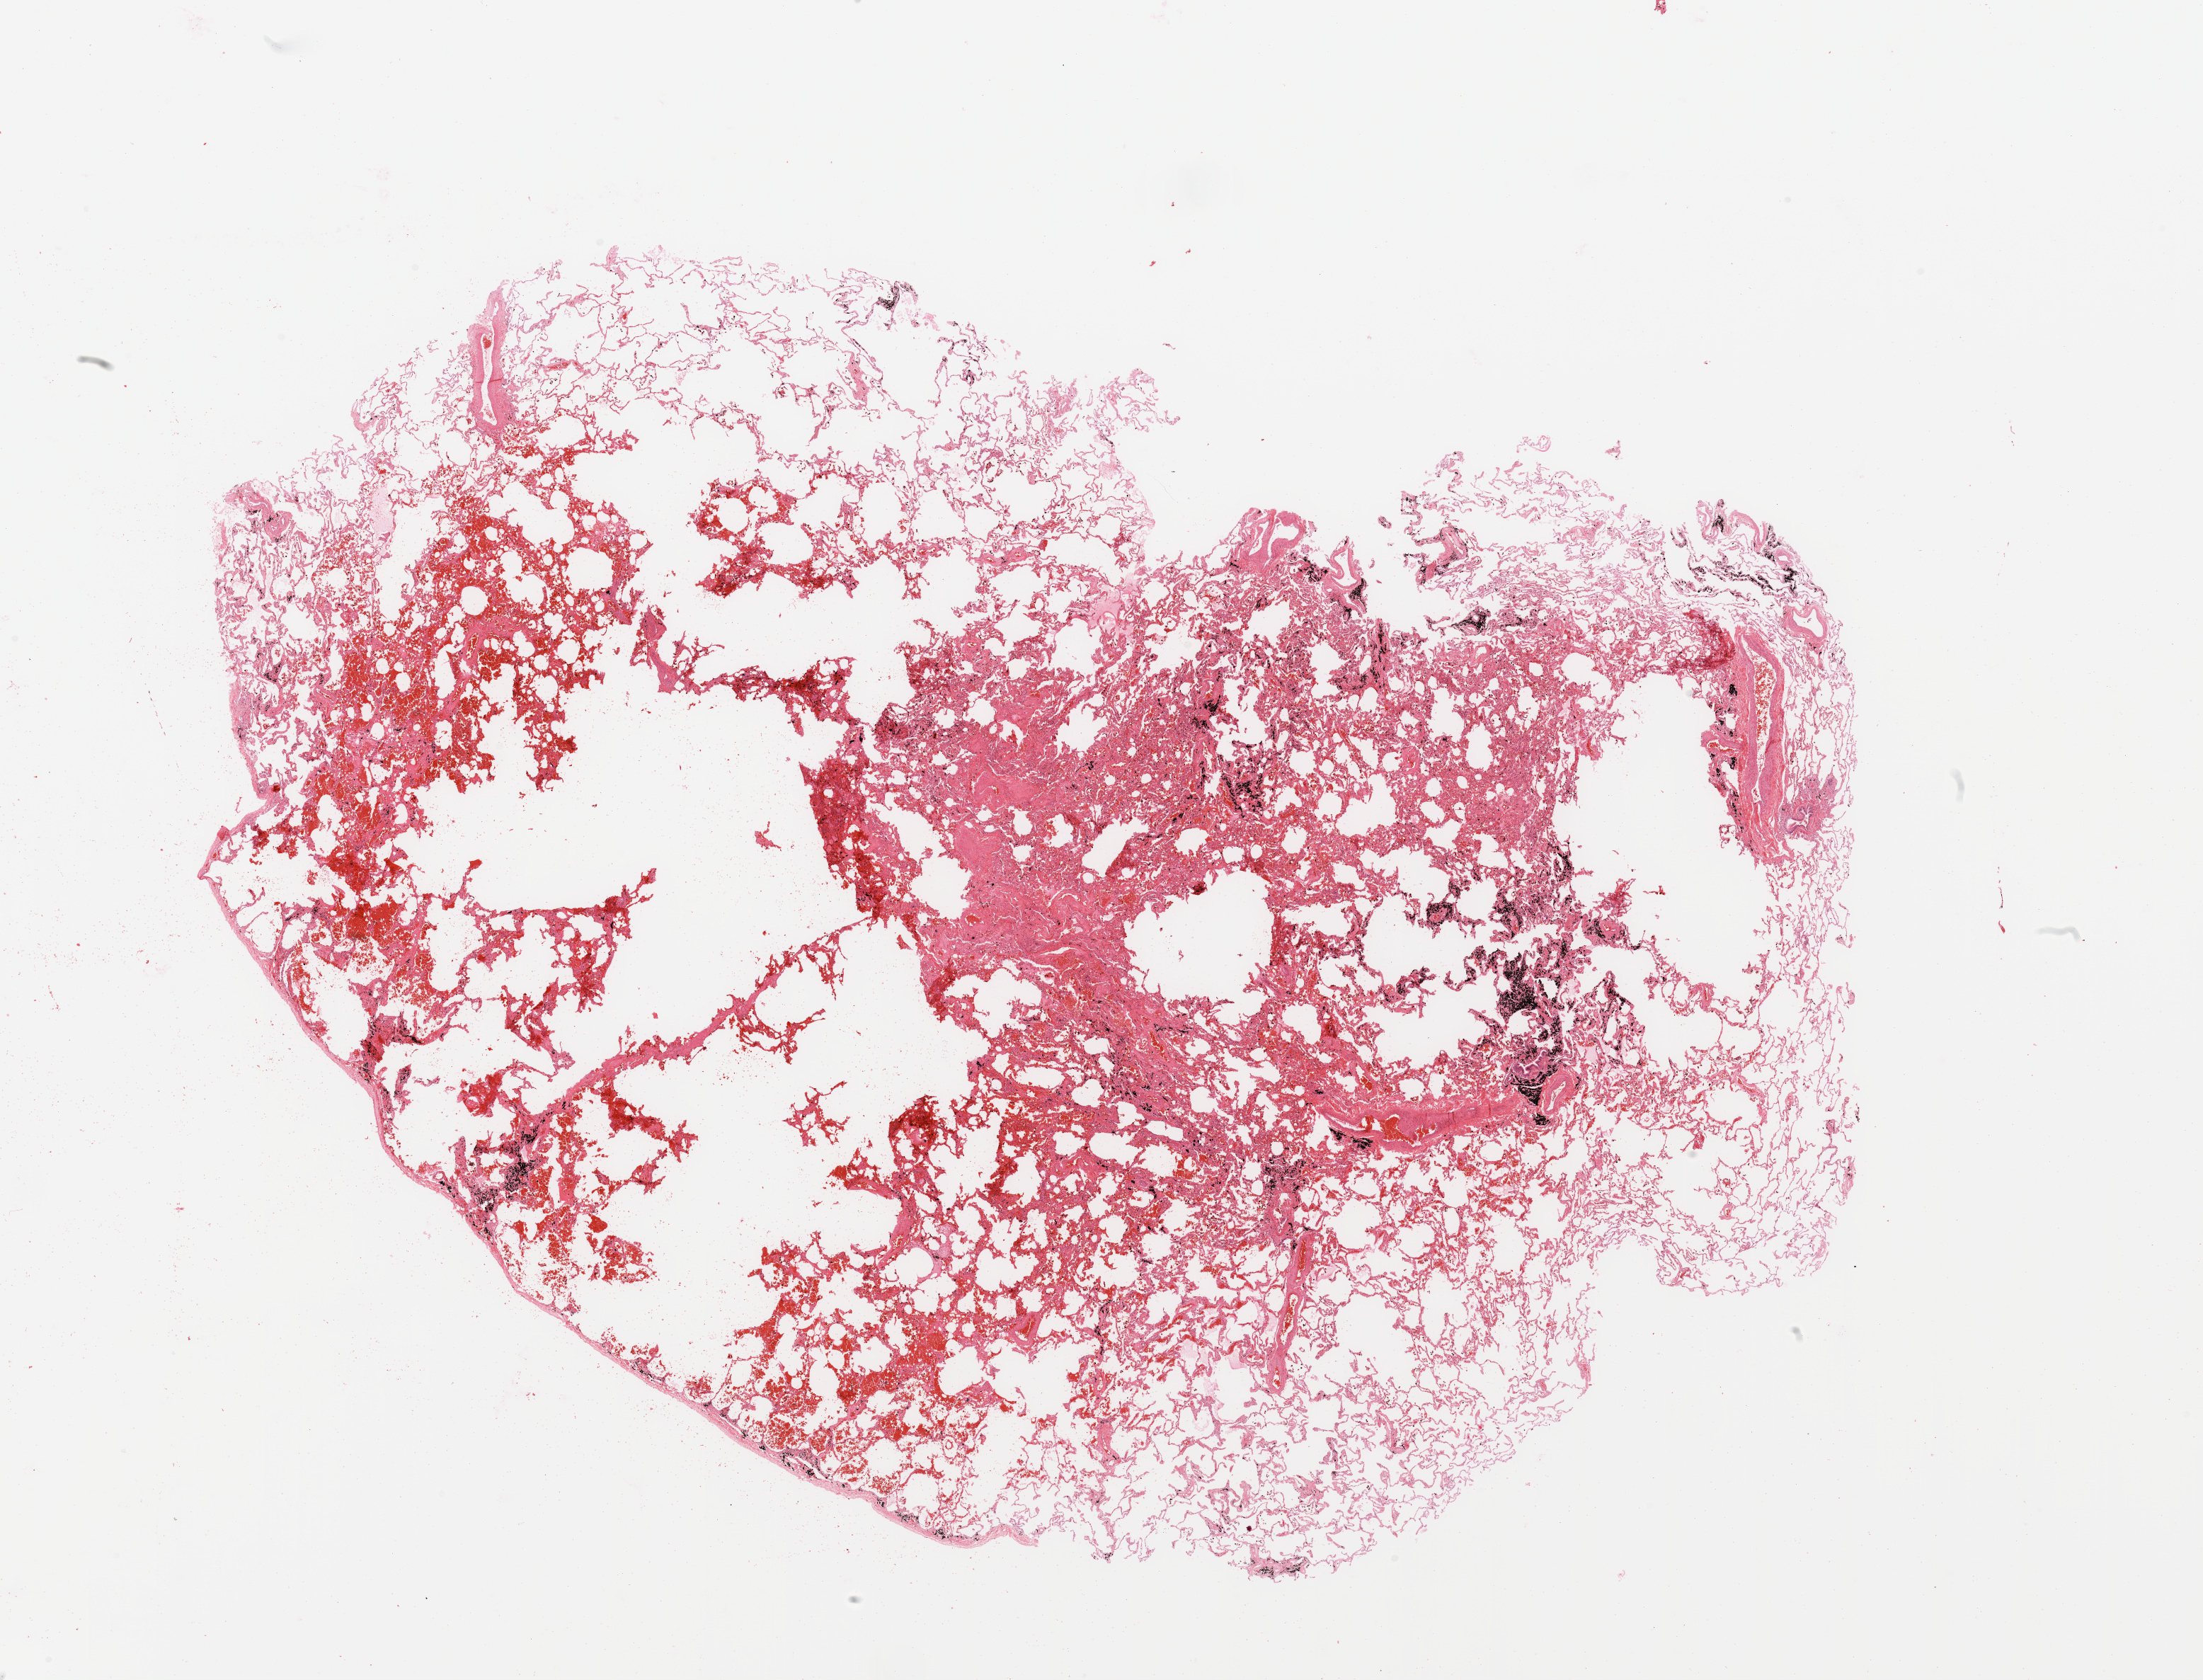
Digitized H&E tissue section (whole slide) — shown as a low-resolution overview of the whole scanned area (about 24.6 x 18.8 mm), normal (non-tumour) tissue sample, sampled site: lung. Male, 64 y/o.
• this section: normal (non-tumour) tissue from the same patient
• patient diagnosis: Adenocarcinoma, NOS